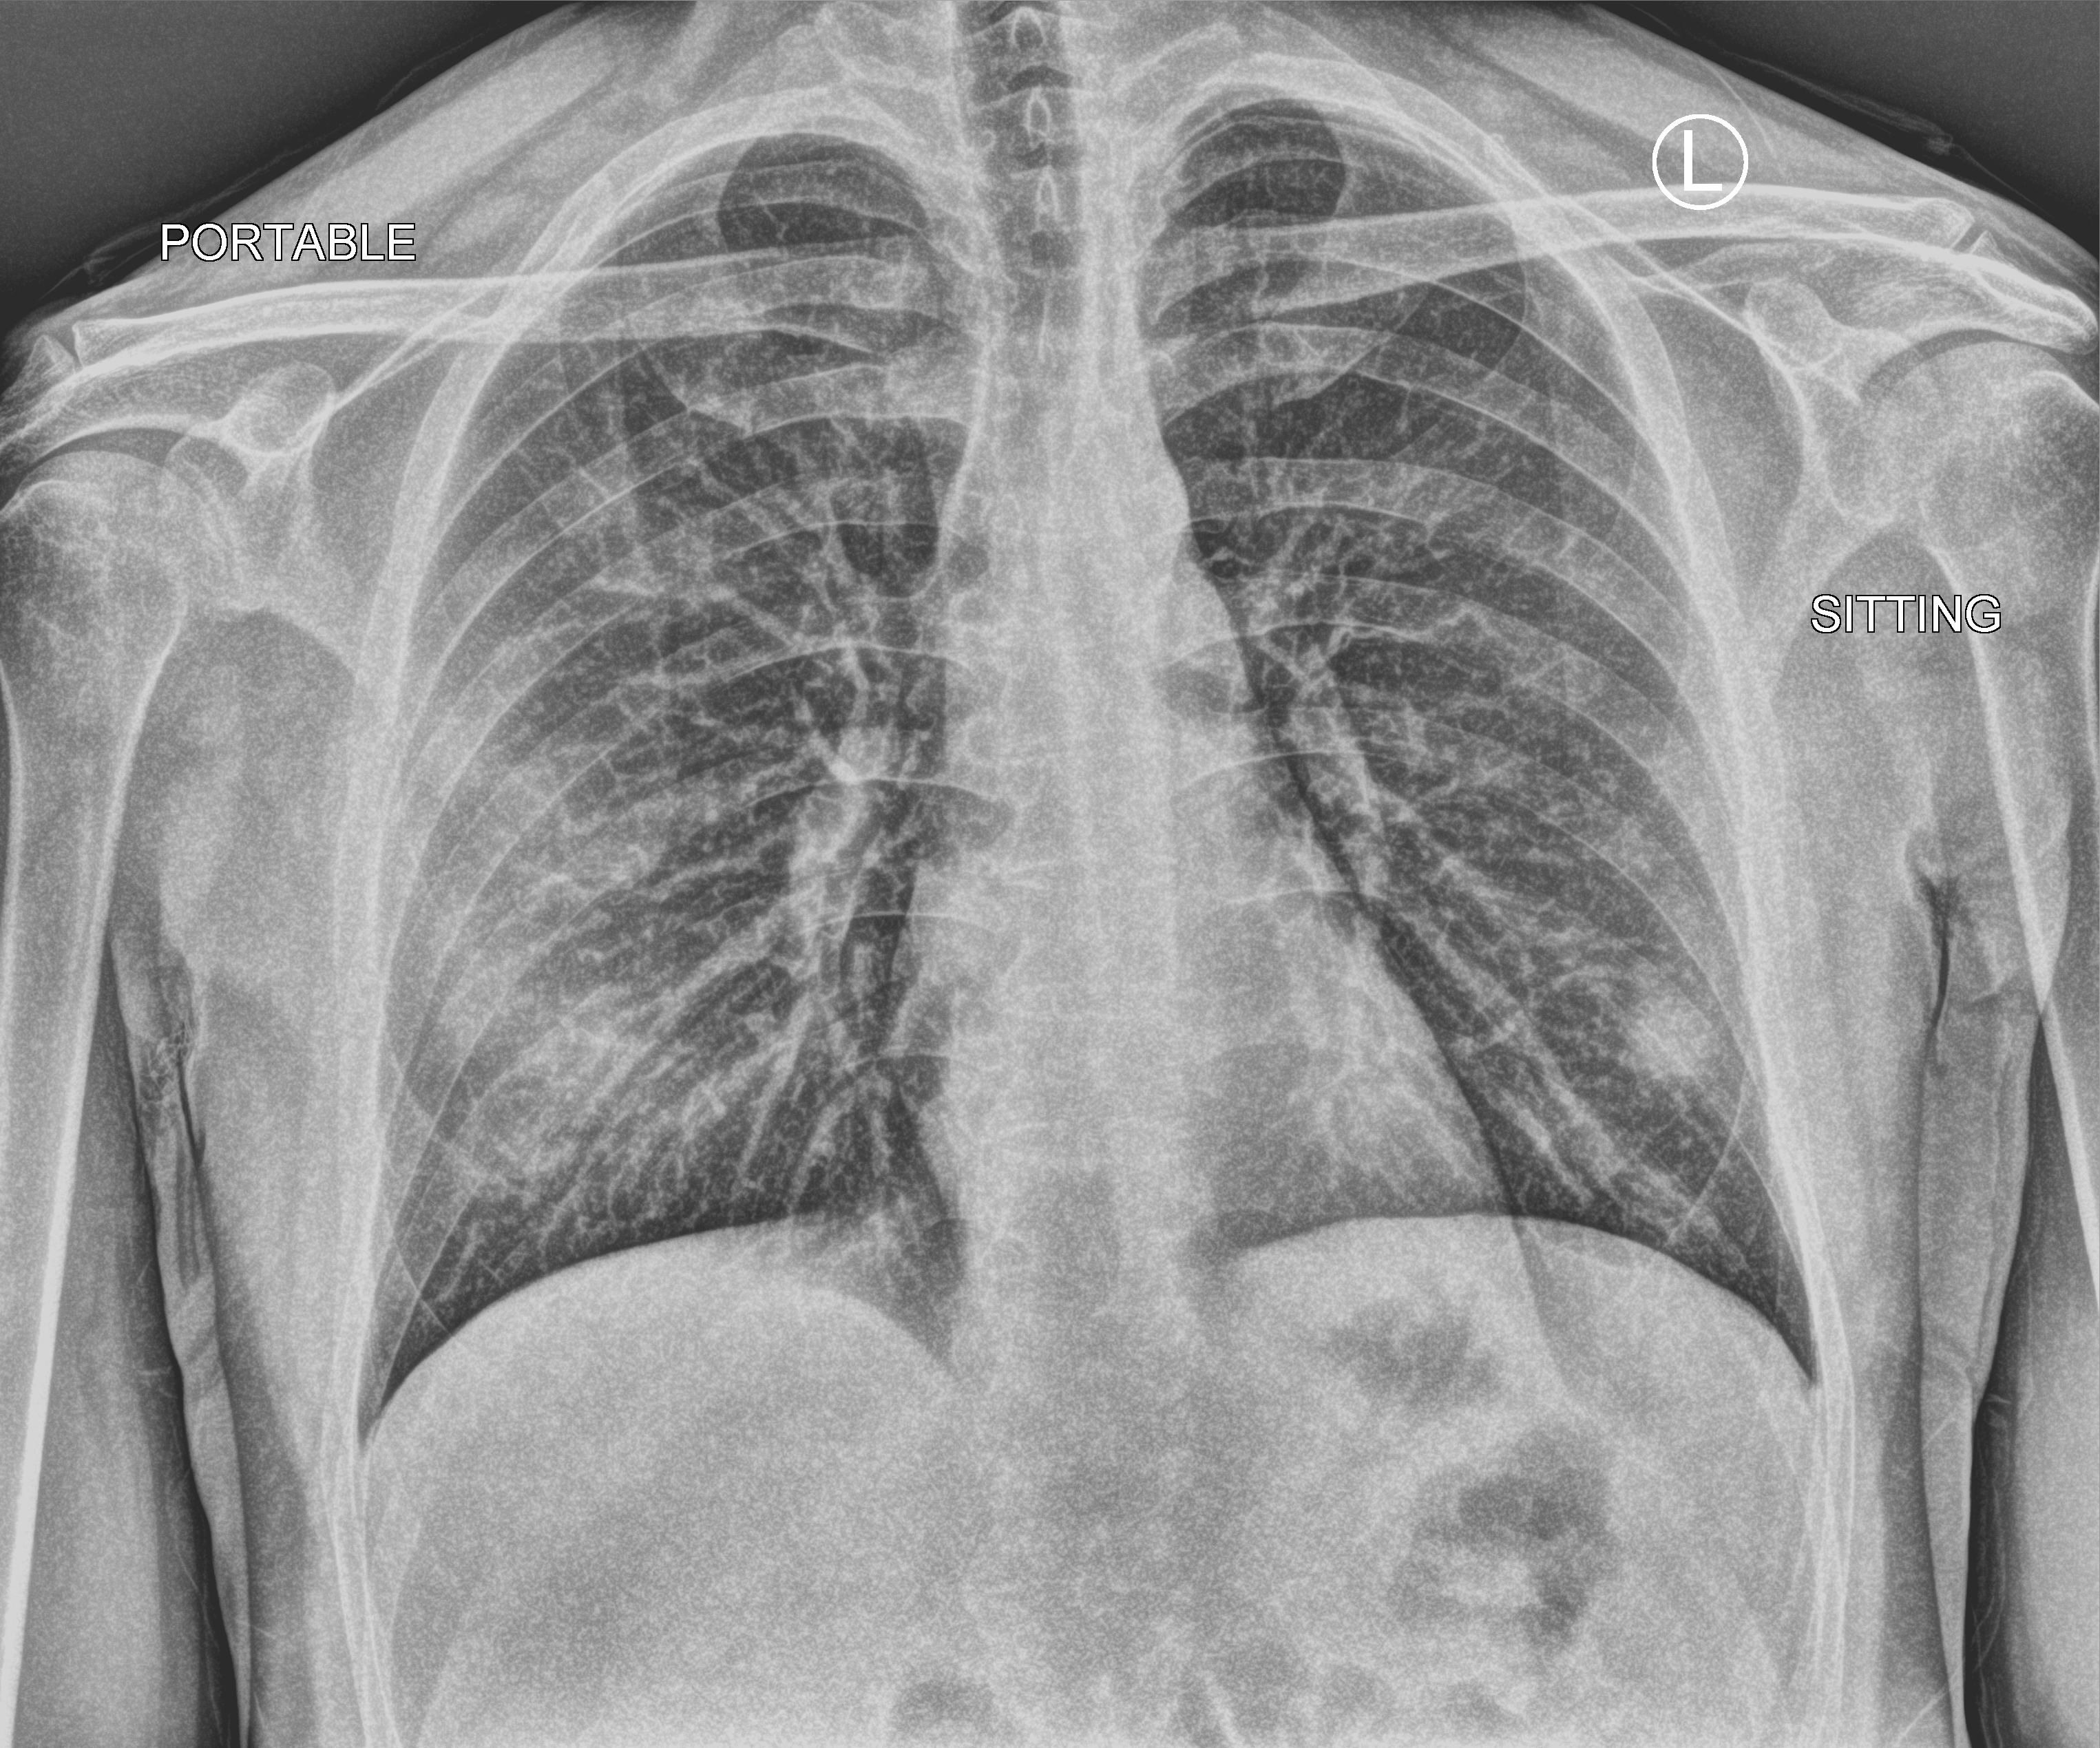
Bedside chest radiograph (computed radiography). Patient hospitalised with COVID-19; male, aged 18–59 years.
From the hospital-stay record, not from the radiograph (when in the stay this image was taken is not recorded): admitted to intensive care during this hospital stay: no; mechanically ventilated during this hospital stay: no; COPD (admission record): no.